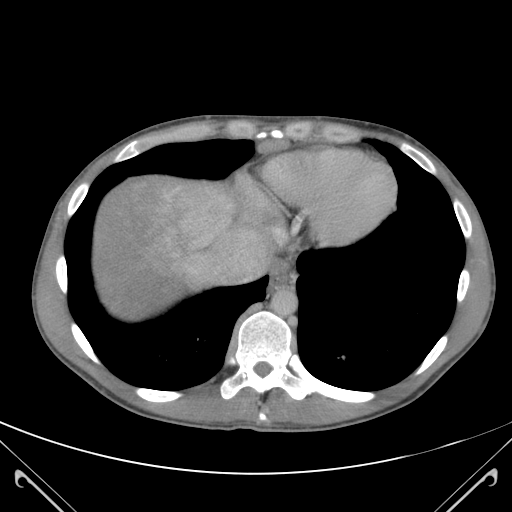
Contrast-enhanced abdominal CT (liver protocol), one axial slice; position 106 of 118 along the scan axis; 120 kVp; soft-tissue window (W 400 / L 40 HU); 3 mm slice thickness; 512 × 512 image matrix, field of view 380 × 380 mm. Case-level facts recorded for this patient, not image findings: diagnosis: hepatocellular carcinoma (patient treated with transarterial chemoembolisation; whether this scan precedes or follows treatment is not stated here); TNM stage (as recorded): Stage-IIIB; Child-Pugh class: A; tumour nodularity: uninodular.
Annotated regions visible in this slice (semi-automatically segmented with operator editing):
- abdominal aorta: bounding box <273,291,296,313> (left, top, right, bottom; pixels)
- liver parenchyma outside the tumour (the mass and vessels are separate outlines, so this box may not span the whole liver): <94,177,251,309>
- liver vessels: <165,188,244,273>